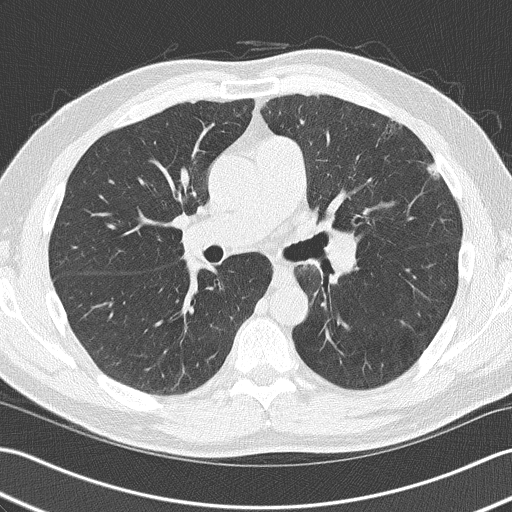
Axial slice from a low-dose chest CT screening exam, baseline annual screen, lung window (W 1500 / L -600 HU), 2 mm slice thickness, lung (sharp) reconstruction kernel (B50f), 512 × 512 image matrix. Male participant, aged 58 years at enrolment. Current smoker at enrolment.
- Lesion marked by an expert reader, box from (x=414, y=152) to (x=460, y=190) px.
- Reader record for this screening exam (exam-level; its link to the box is not recorded): non-calcified nodule or mass ≥4 mm, lingula, 10 × 6 mm, mixed attenuation.
- Lung cancer was diagnosed 258 days after this screen: squamous cell carcinoma, NOS, lingula, poorly differentiated (G3), stage IIIB (AJCC 6th edition).